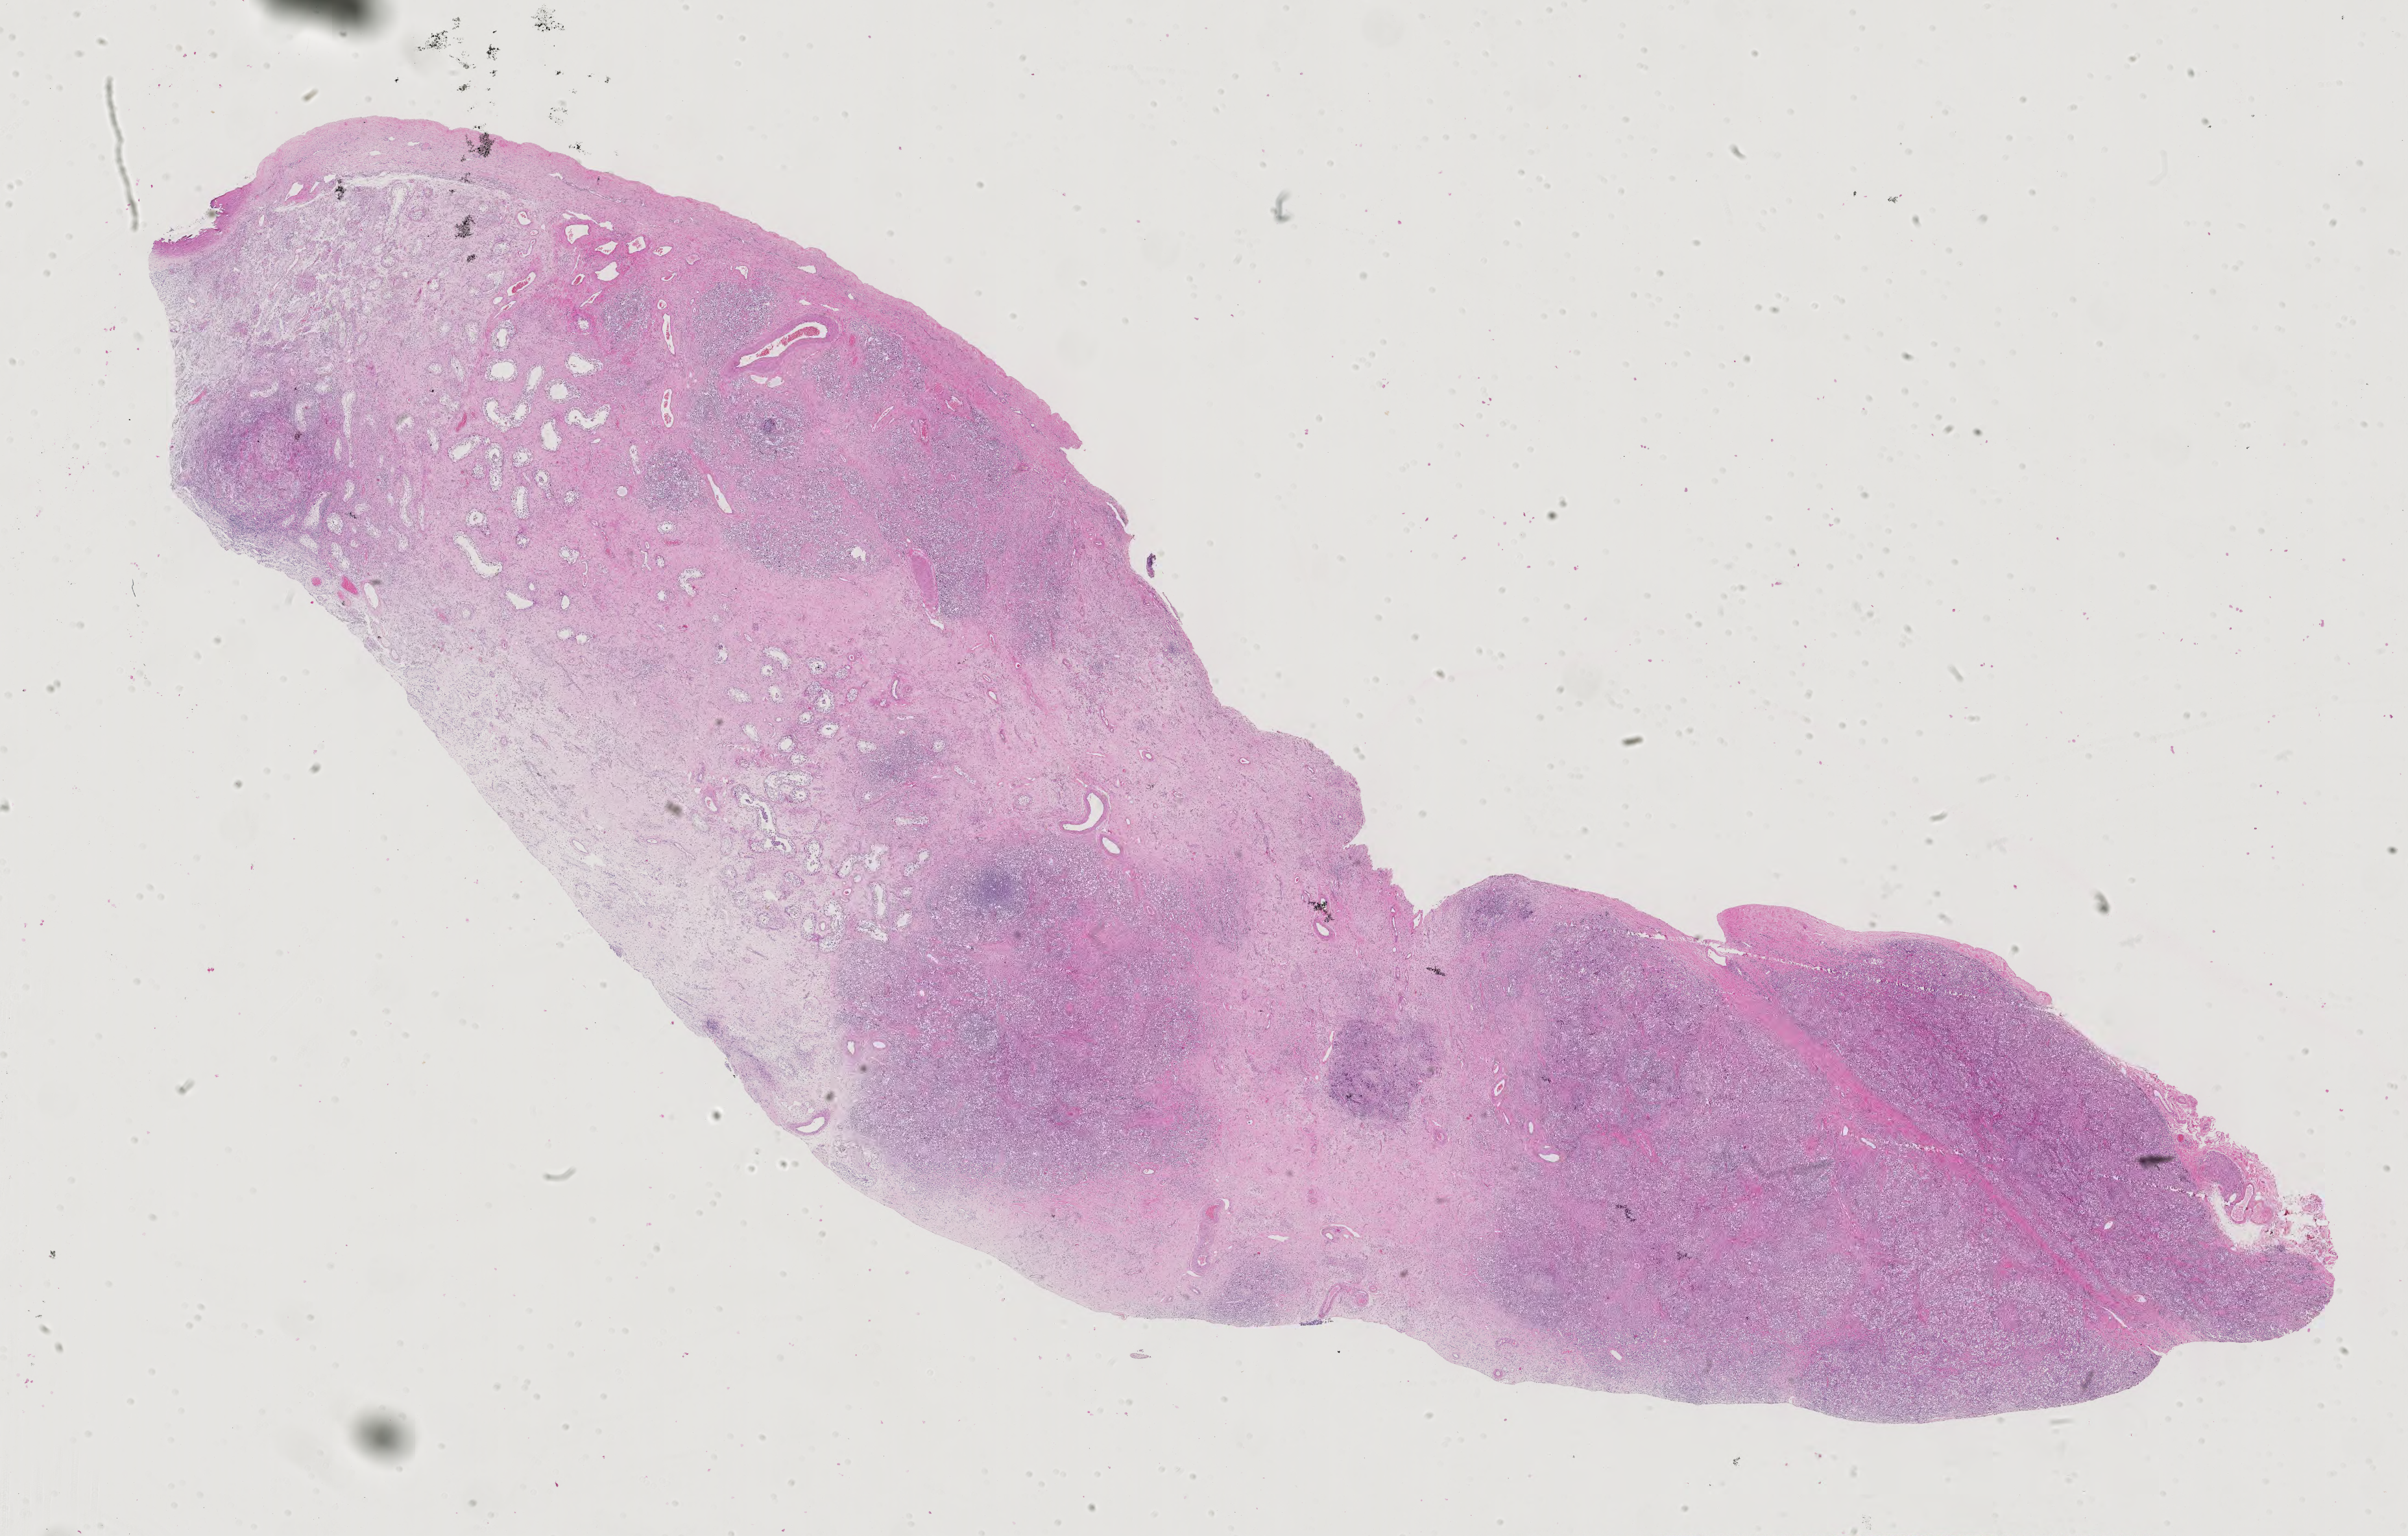
Whole-slide histology image, Hematoxylin and eosin (H&E) stained, shown as a low-resolution overview of the whole scanned area (about 27.0 x 17.3 mm); formalin-fixed paraffin-embedded (FFPE) diagnostic section; sample: primary tumour, testis. Male patient; age at initial diagnosis 30 years.
Histologic diagnosis: Seminoma, NOS. AJCC pathologic stage: IS (5th edition). TNM: T1 N0 M0.